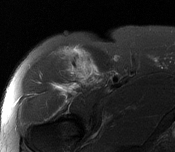
MRI of an extremity soft-tissue mass, one axial slice; slice 113 of 116 in the series (ordered by position); T2-weighted fat-saturated; MR volume resampled by the dataset authors to the PET/CT grid (not the native acquisition matrix); 3.27 mm slice thickness; 175 × 152 image matrix, field of view 171 × 148 mm. Male patient. Case-level facts recorded for this patient, not image findings: histological type: pleiomorphic leiomyosarcoma; grade: intermediate; site of the primary tumour: right thigh.
Annotated regions visible in this slice (expert contour drawn on MRI and transferred to this co-registered scan by the dataset authors):
- gross tumour volume including surrounding oedema: bounding box [x1, y1, x2, y2] px = [70, 54, 96, 84]